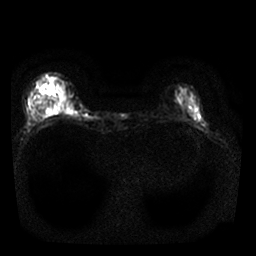
Breast MRI, one axial slice. Slice 5 of 25 in the series (ordered by position). Diffusion-weighted series; image 2 of 4 stored at this slice position (different b-values; order by instance number). 1.5 T. 4 mm slice thickness. 256 × 256 image matrix, field of view 310 × 310 mm. Female patient.
Annotated regions visible in this slice (manually delineated by an expert):
- tumour on diffusion-weighted imaging: bounding box [x1, y1, x2, y2] px = [65, 101, 71, 109]